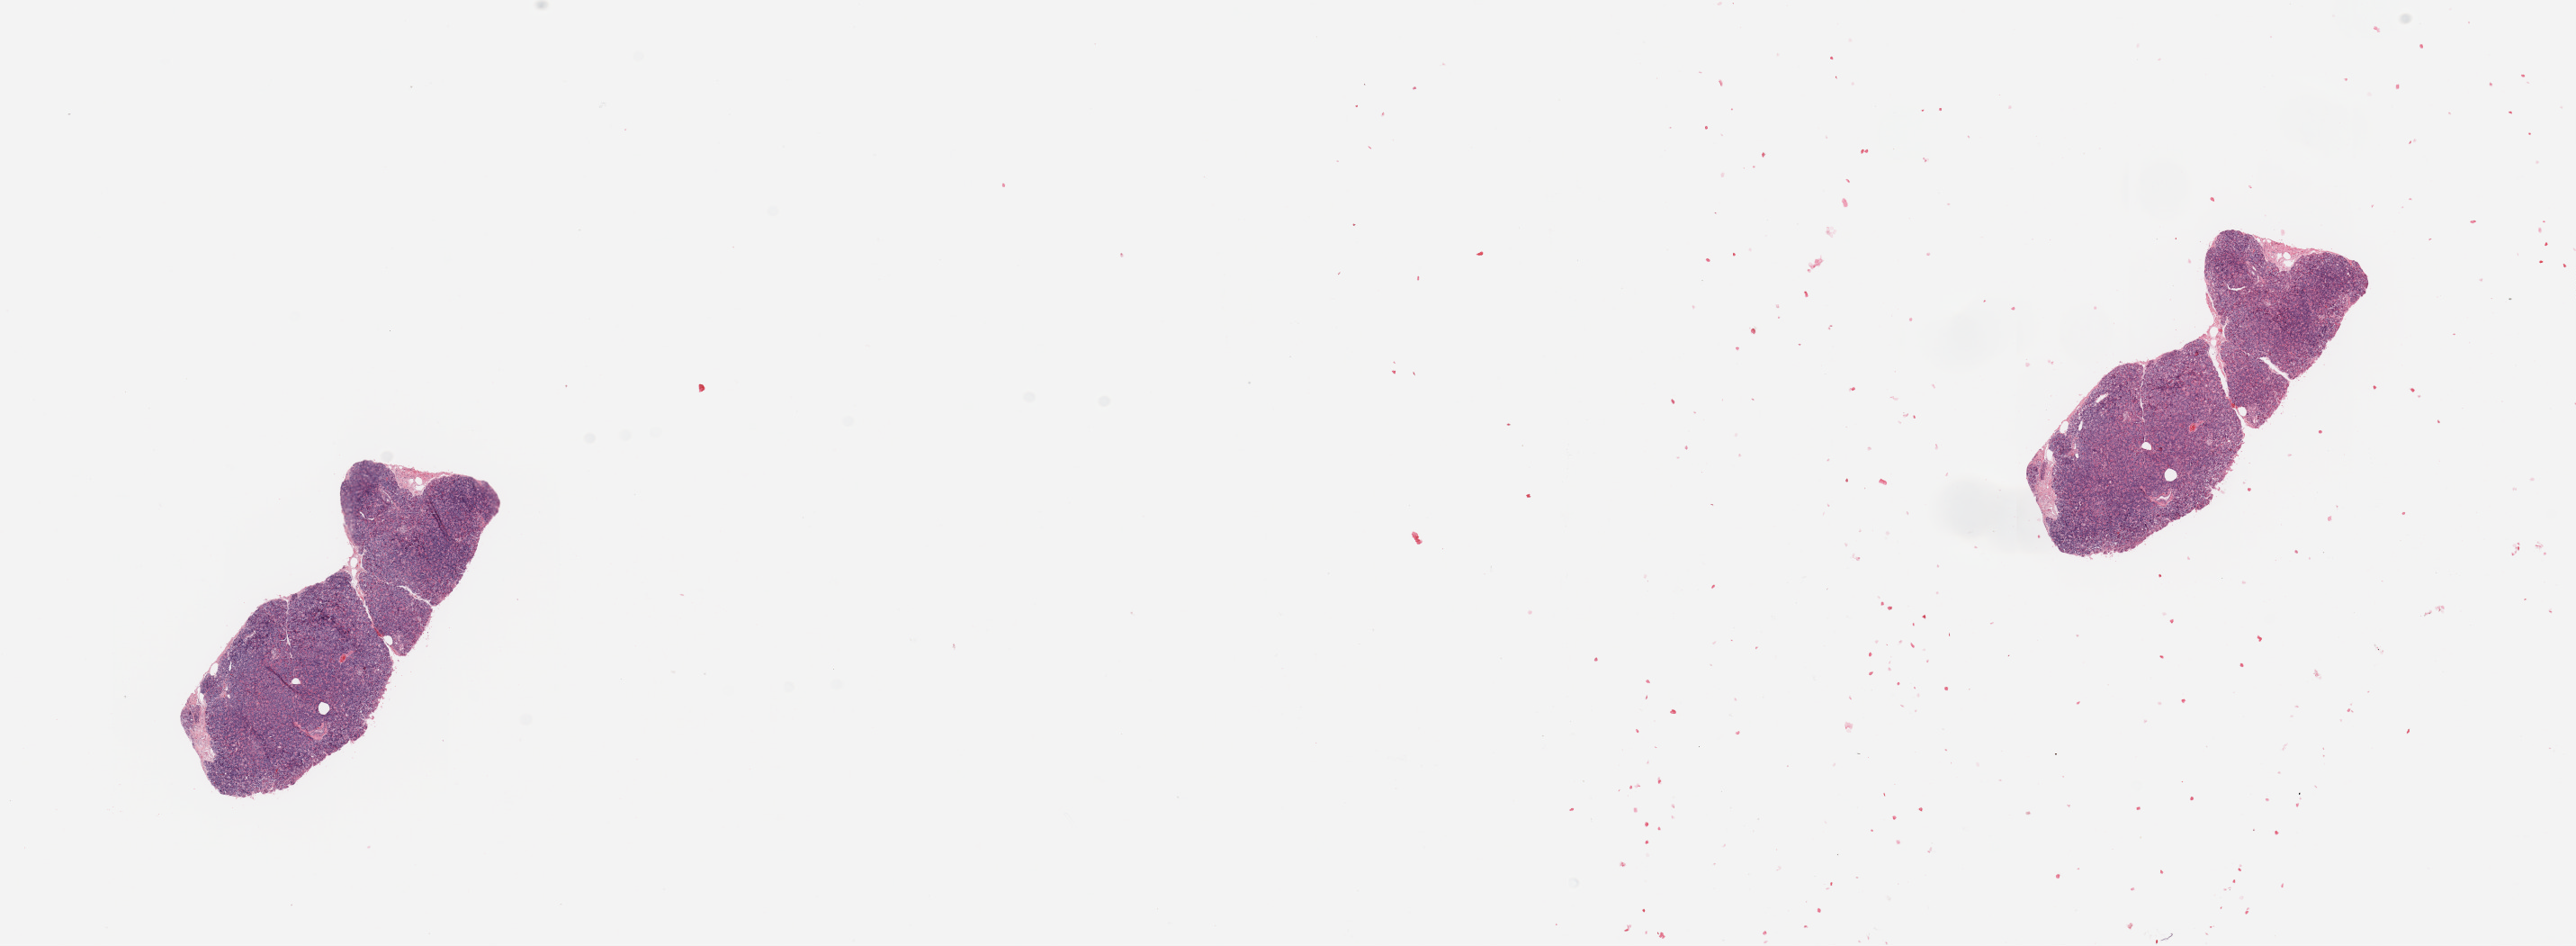
Hematoxylin and eosin (H&E) stained whole-slide image, a low-resolution overview of the entire scanned area, about 22.6 x 8.3 mm; normal (non-tumour) tissue sample, sampled site: pancreas. Patient: male, age 71 years.
• this section: normal (non-tumour) tissue from the same patient
• patient diagnosis: Infiltrating duct carcinoma, NOS